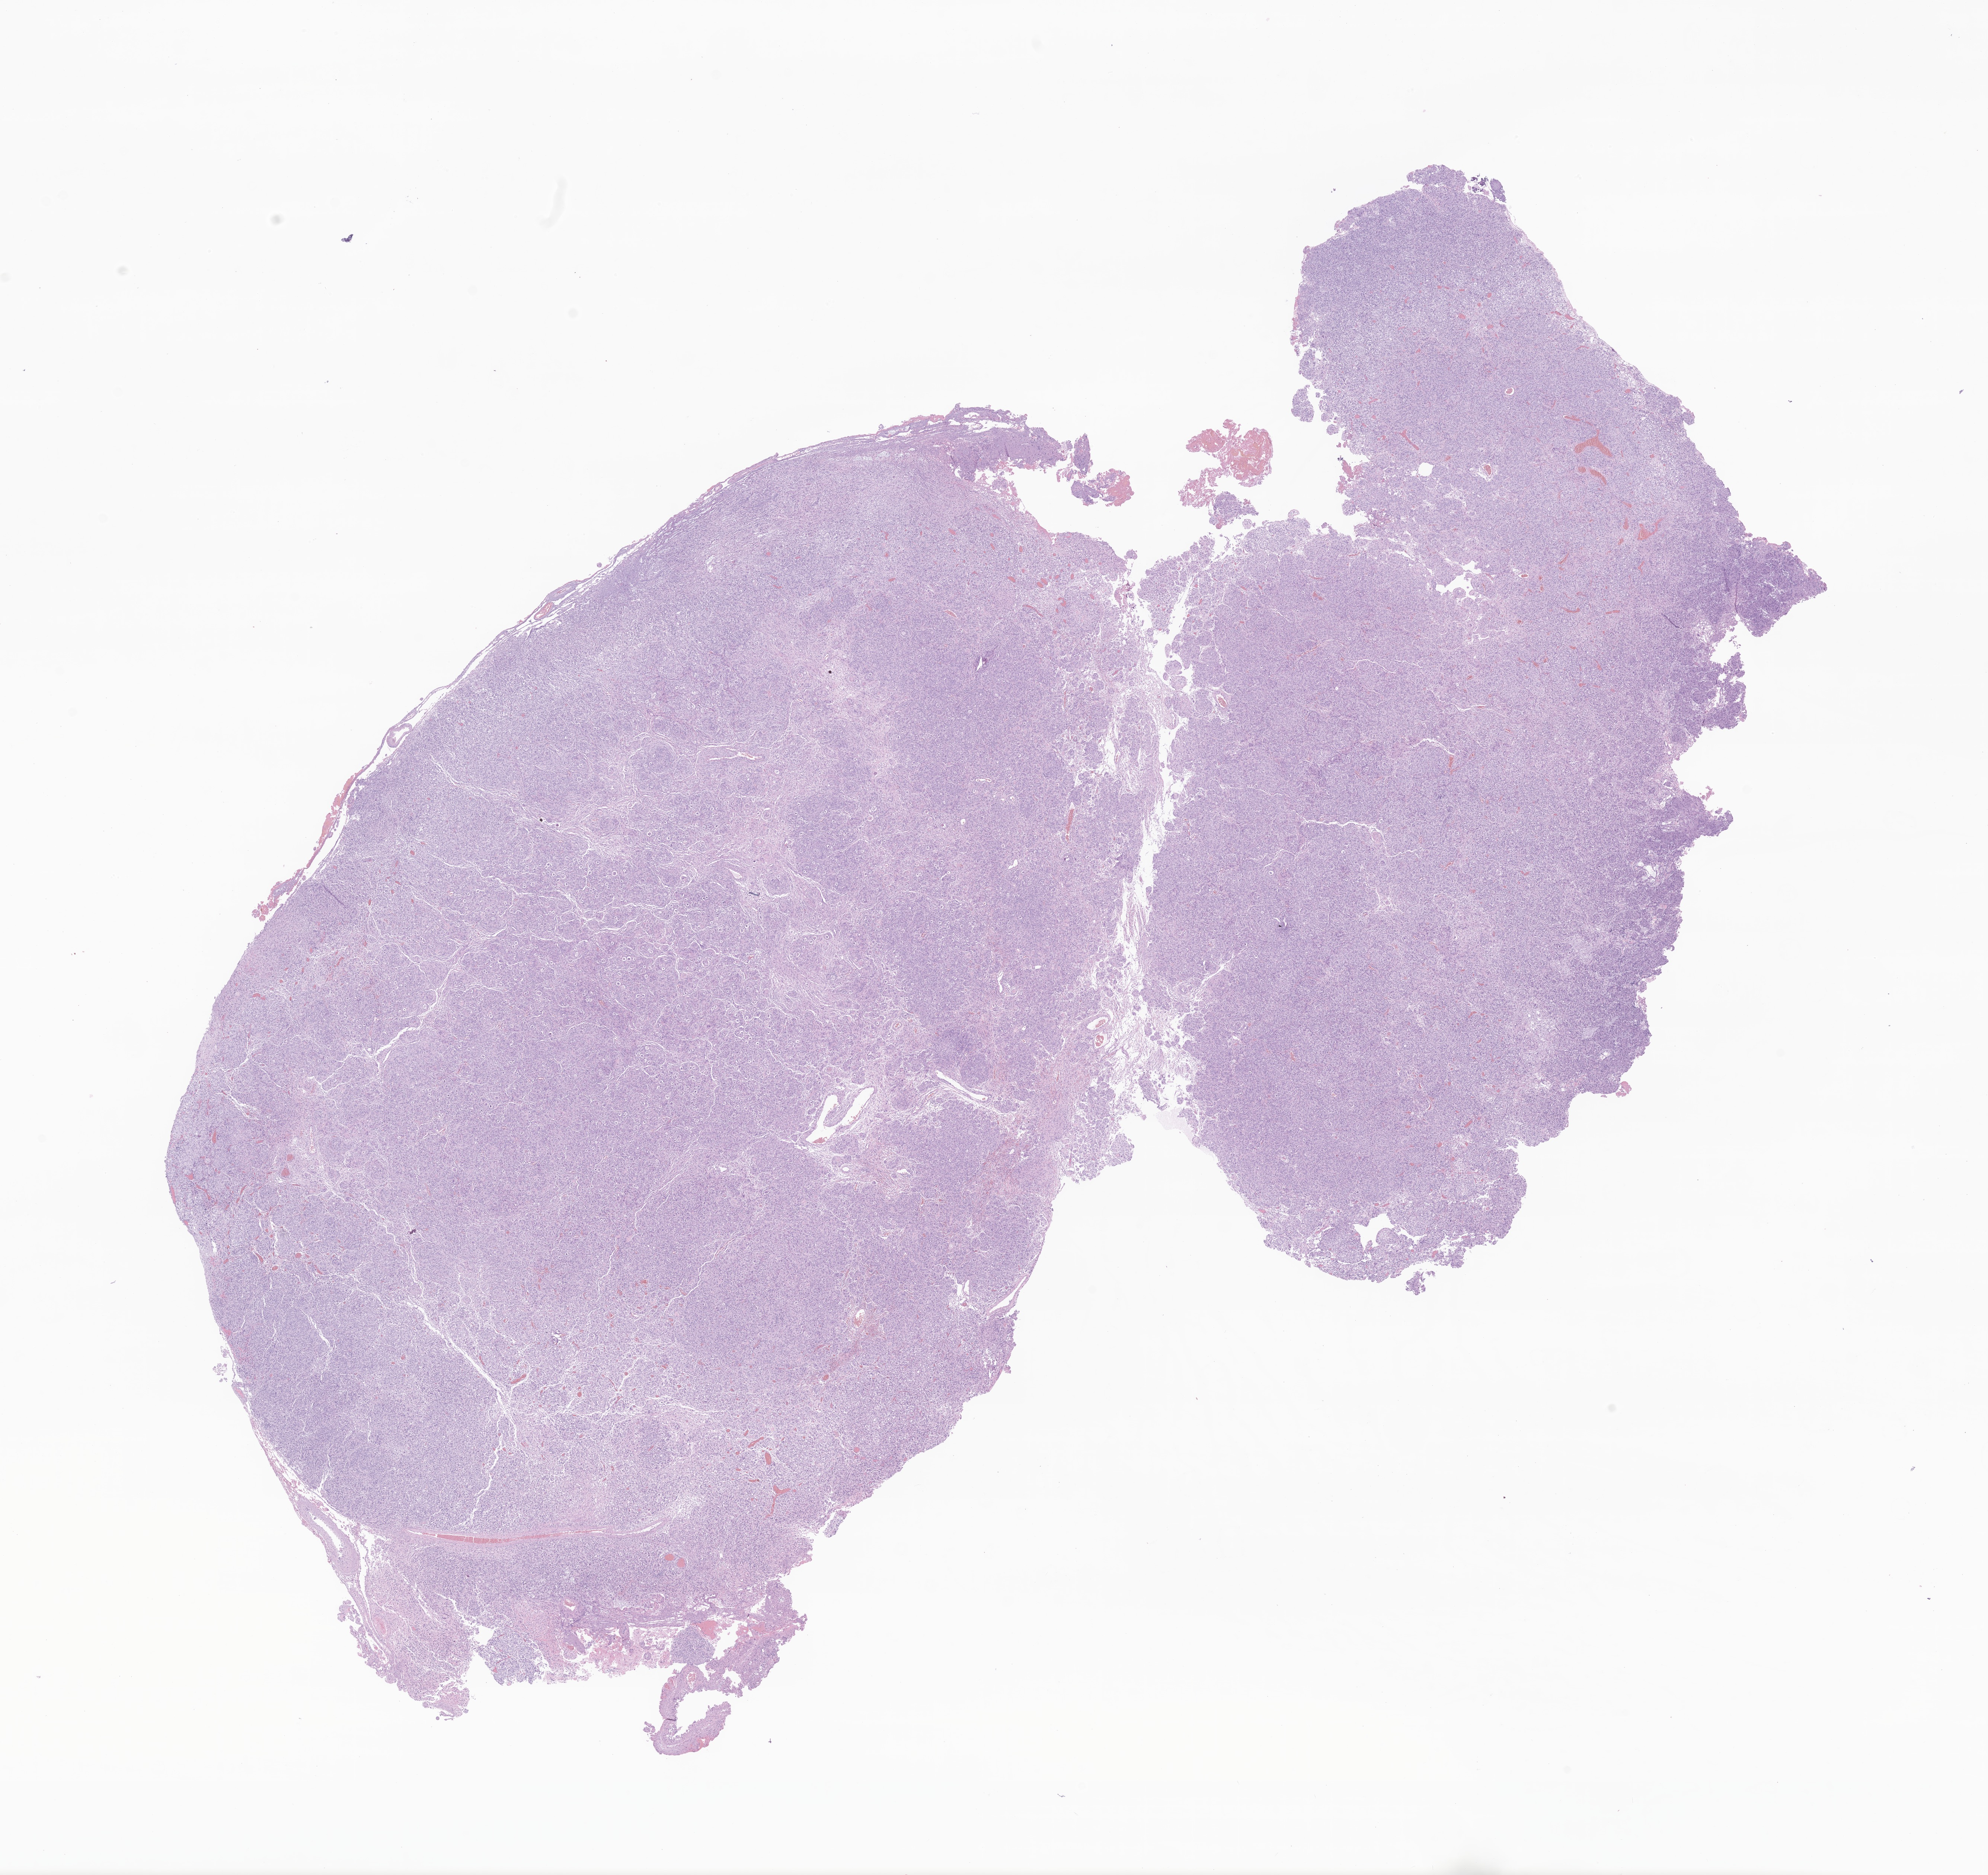
Digitized hematoxylin and eosin (H&E)-stained section of tumor tissue from the temporal lobe — shown as a low-resolution overview of the whole scanned area (about 22.5 x 21.2 mm), formalin-fixed paraffin-embedded section. Male patient, age 111 months (9 years 3 months).
Diagnosis (ICD-O-3 morphology term): Meningothelial meningioma.